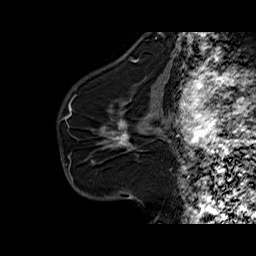
Breast MRI (dynamic contrast-enhanced), one sagittal slice; position 39 of 60 along the scan axis; dynamic contrast-enhanced series, time point 2 of 6 at this slice position (early post-contrast); 1.5 T; TE 6.3 ms, TR 32.5 ms; 4 mm slice thickness; 256 × 256 image matrix, field of view 200 × 200 mm. Female patient. Case-level facts recorded for this patient, not image findings: setting: breast cancer imaged before/during neoadjuvant chemotherapy; receptor status: HR-positive, HER2-negative.
Outlined on this slice (semi-automatic segmentation, software-assisted and operator-edited):
- analysis volume of interest (the breast-tissue region the enhancement analysis was run in; not a lesion): bounding box [x1, y1, x2, y2] px = [94, 103, 161, 164]
- tumour enhancement mask (voxels above the 100 % enhancement threshold inside the analysis volume of interest): [113, 120, 129, 145]